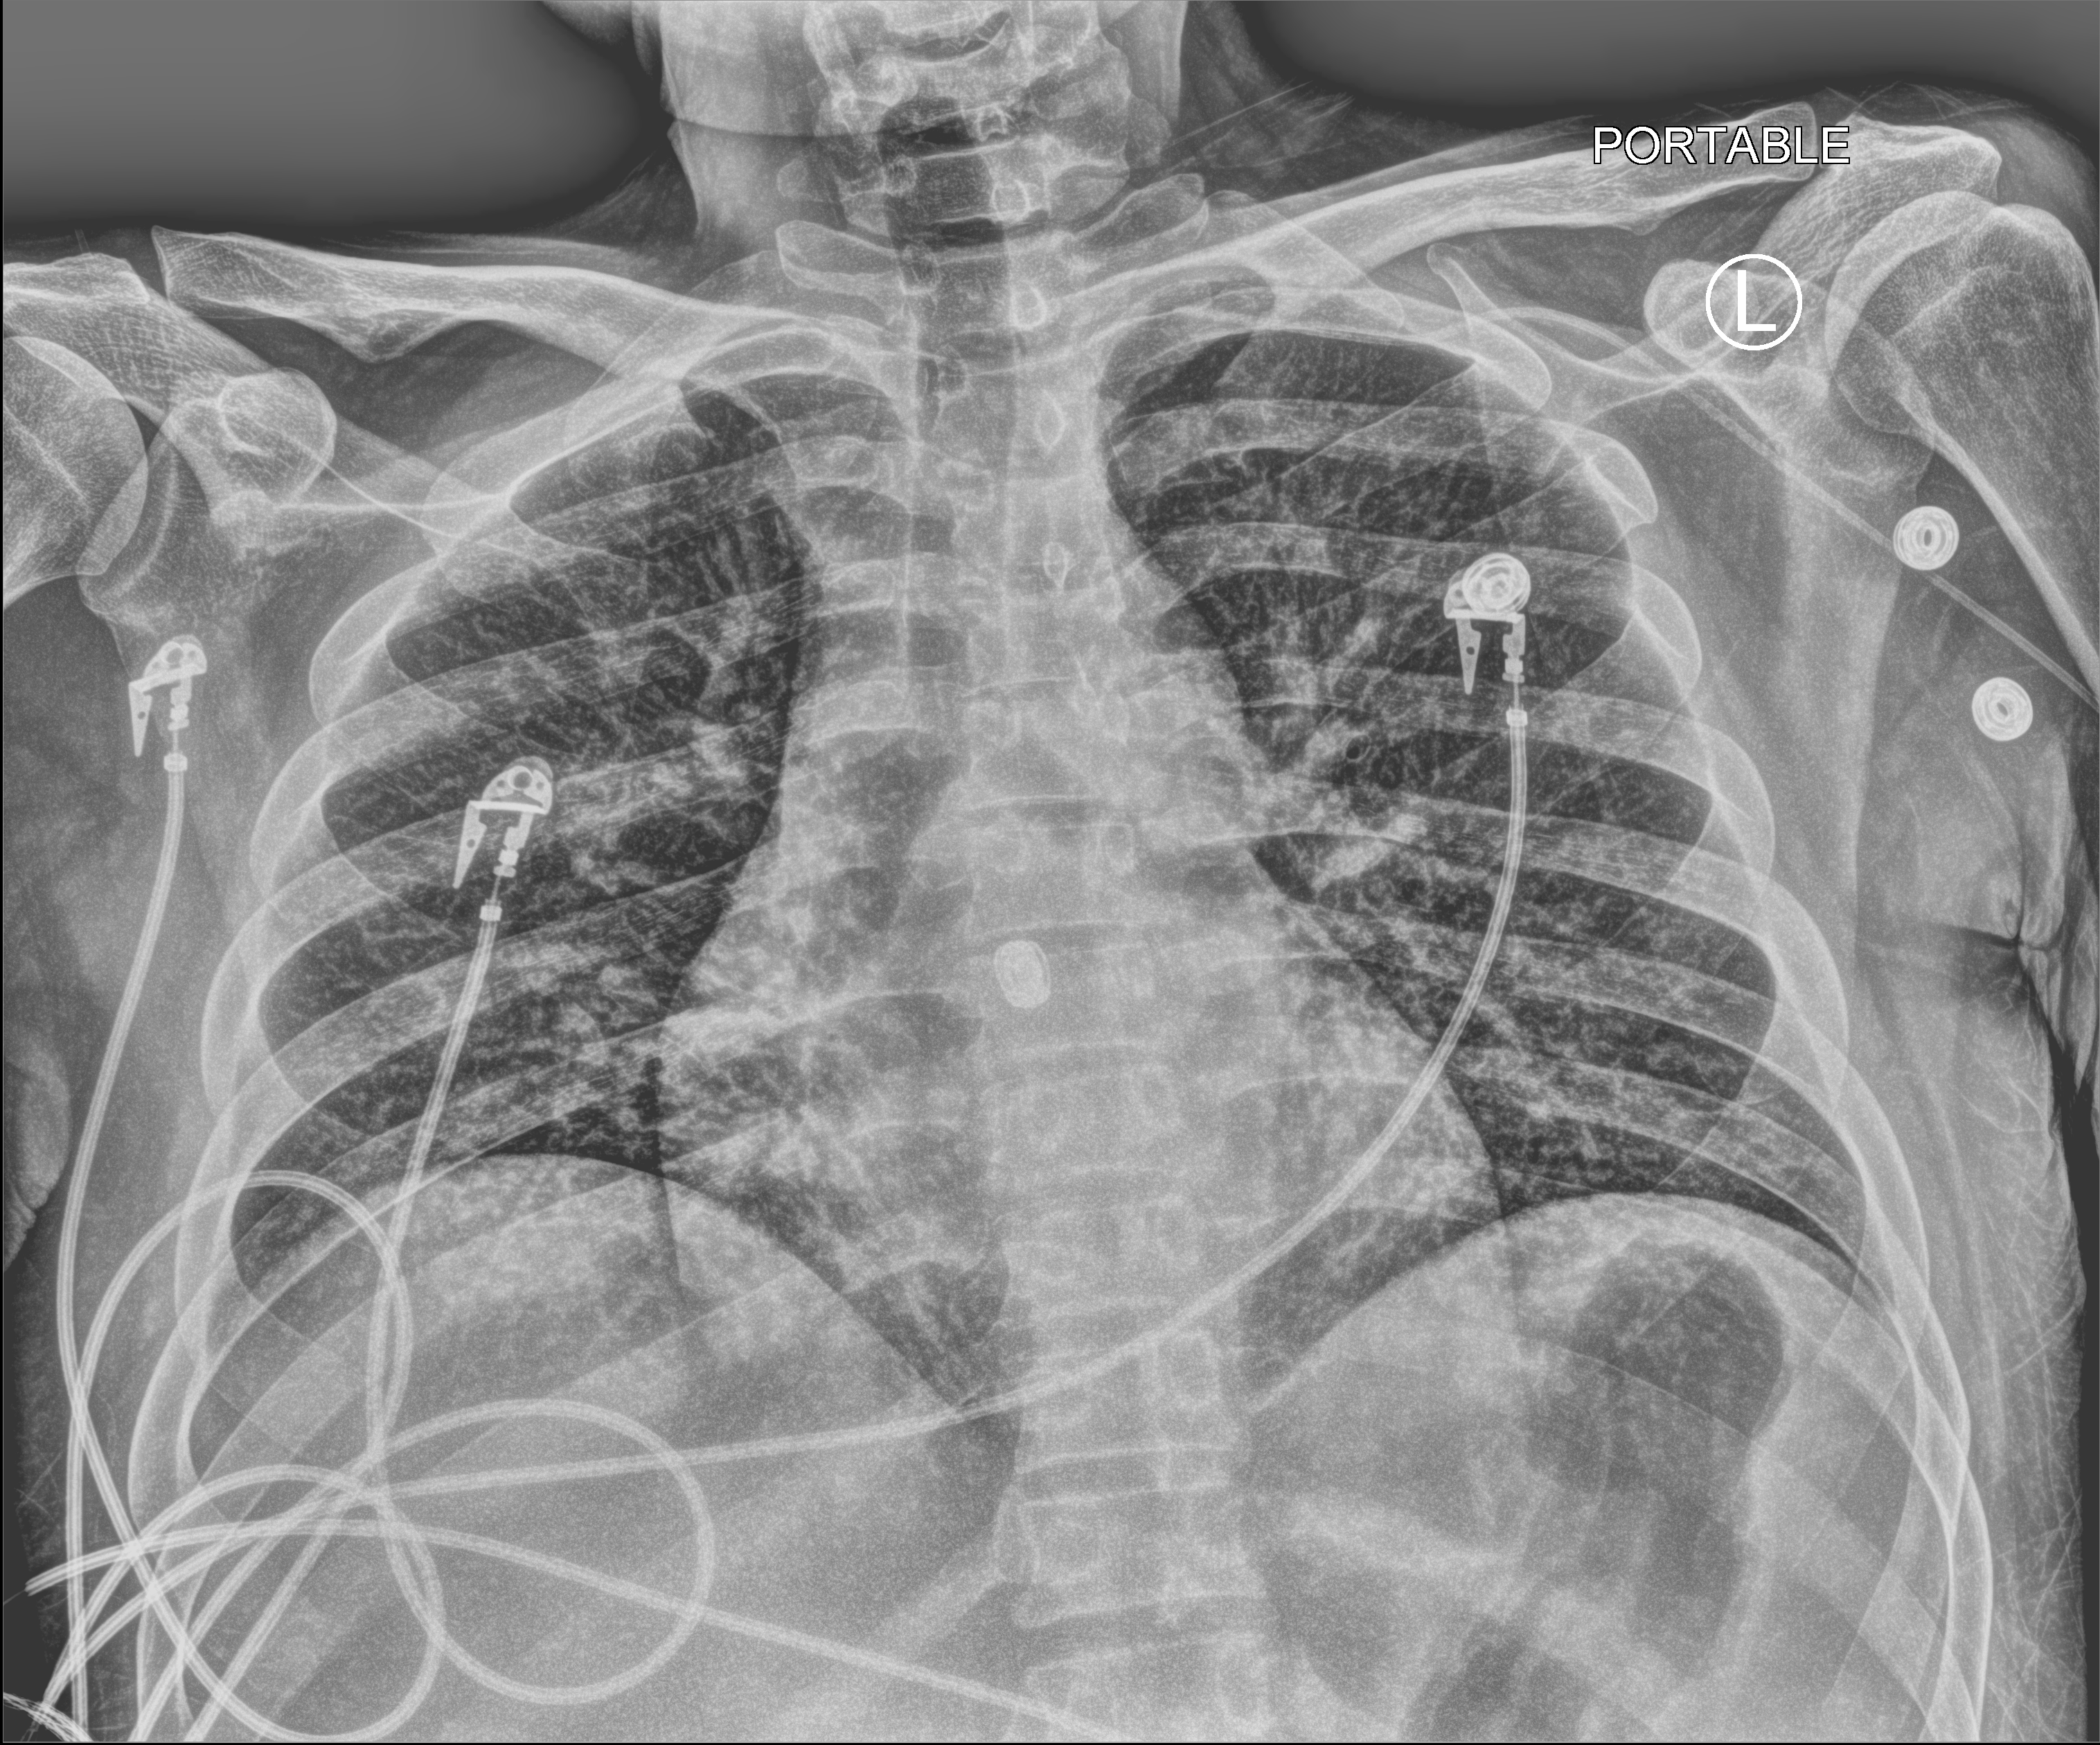
Chest X-ray (portable); anteroposterior (AP) projection. Patient hospitalised with COVID-19; male, aged 18–59 years.
Admission-level facts for this patient (not findings on this image; timing relative to this image not recorded): mechanically ventilated during this hospital stay: yes.